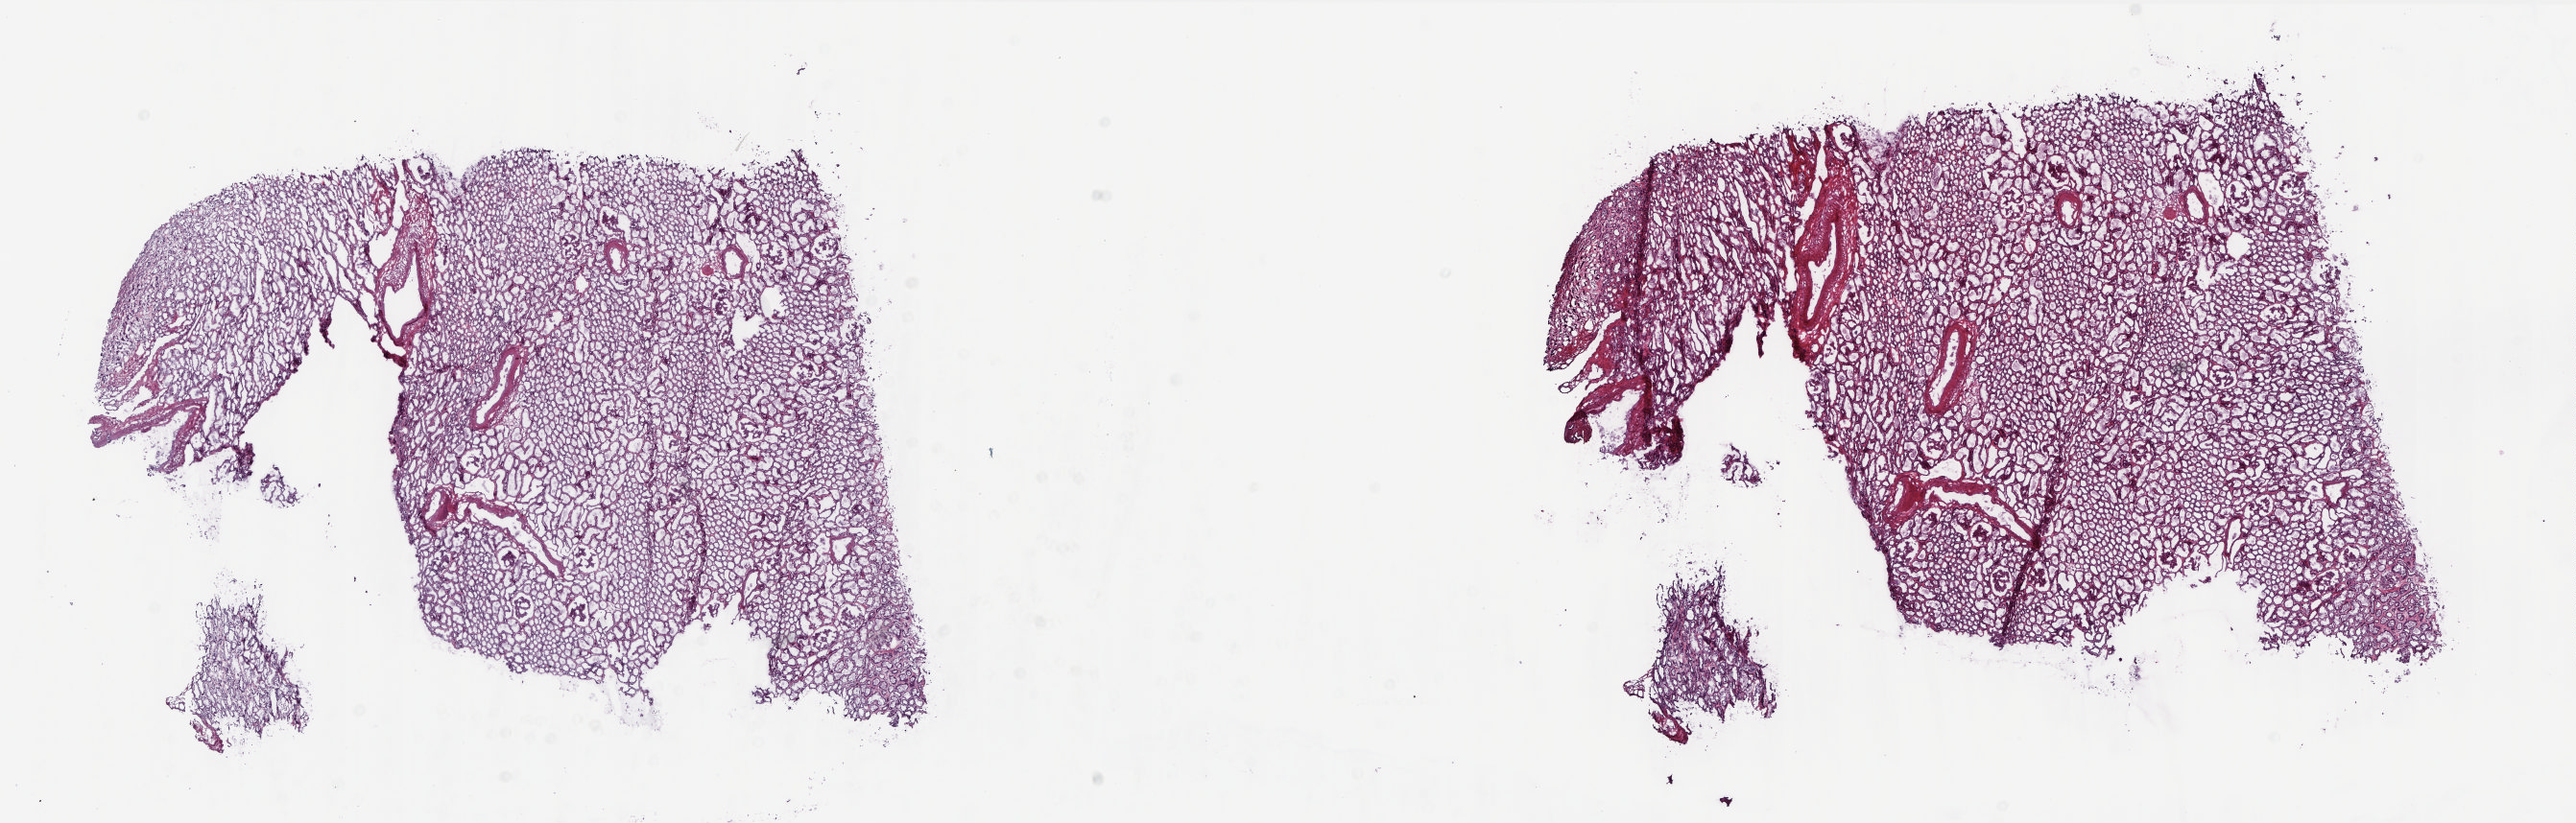
H&E whole-slide image, whole scanned area (about 21.6 x 6.9 mm) shown as a low-resolution overview, frozen section from the top of the tissue portion, sample: solid tissue normal (non-tumour tissue), kidney. Female, age 54 years at initial diagnosis. Slide review estimates, as recorded: tumour cells 0%, tumour nuclei 0%, normal cells 100%, stromal cells 0%, necrosis 0%. Inflammatory infiltration, as recorded: lymphocyte infiltration 1%, monocyte infiltration 0%, neutrophil infiltration 0%.
This section: solid tissue normal sample (biorepository sample class). Patient diagnosis: Papillary adenocarcinoma, NOS.